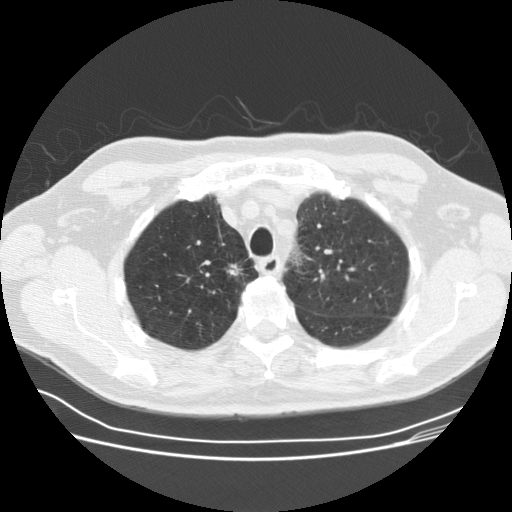
Axial slice from a low-dose chest CT screening exam; third annual screen; lung window (W 1500 / L -600 HU); 2.5 mm slice thickness; slice 127 of 164 in the series; 512 × 512 image matrix, field of view 360 × 360 mm. Male participant, aged 69 years at enrolment. Current smoker at enrolment.
• Expert-annotated lung lesion, bounding box (x1, y1, x2, y2) in pixels: (220, 256, 255, 290).
• Reader record for this screening exam (exam-level; its link to the box is not recorded): non-calcified nodule or mass ≥4 mm, right upper lobe, 12 × 10 mm, spiculated (stellate) margins, soft tissue attenuation, pre-existing on the prior screen: yes; interval growth: yes.
• Lung cancer was diagnosed 36 days after this screen: squamous cell carcinoma, NOS, right upper lobe, moderately differentiated (G2), stage IA (AJCC 6th edition), 9 mm at pathology.